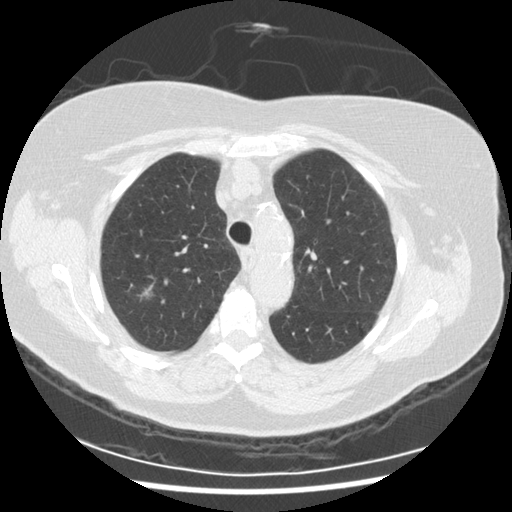
Axial slice from a low-dose chest CT screening exam, third screening round (two years after baseline), lung window (W 1500 / L -600 HU), slice 57 of 254 in the series, 512 × 512 image matrix. Female participant, aged 72 years at enrolment.
Expert-annotated lung lesion, box from (x=130, y=279) to (x=163, y=310) px. Screening reader's record for this exam (one nodule recorded; not confirmed to be the boxed lesion): non-calcified nodule or mass ≥4 mm, right upper lobe, 9 × 8 mm, poorly defined margins, ground glass attenuation, pre-existing on the prior screen: no. Official screen result: positive, other. Participant outcome: lung cancer diagnosed 121 days after this screen — squamous cell carcinoma, NOS, right upper lobe, poorly differentiated (G3), stage IIIA (AJCC 6th edition), 22 mm at pathology.